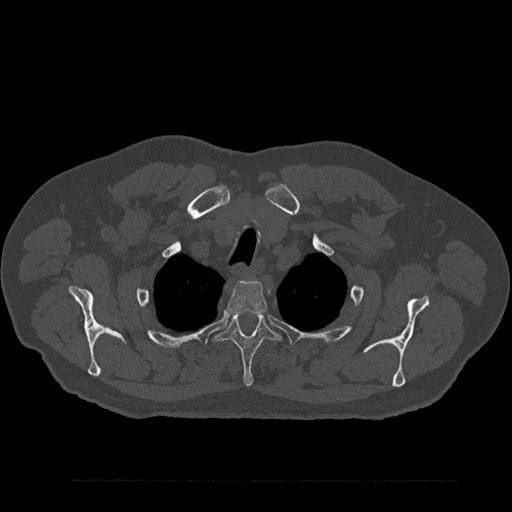
CT including the spine, one axial slice; position 694 of 797 along the scan axis; reconstruction kernel Br40s/3; bone window (W 1800 / L 400 HU); 0.5 mm slice thickness; 512 × 512 image matrix, field of view 430 × 430 mm. Male patient, age 61 years. Case-level facts recorded for this patient, not image findings: primary cancer: prostate.
Outlined on this slice (semi-automatically segmented with operator editing):
- T2 vertebra: bounding box (x1, y1, x2, y2) in pixels: (224, 280, 268, 316)
- T3 vertebra: (216, 314, 280, 387)